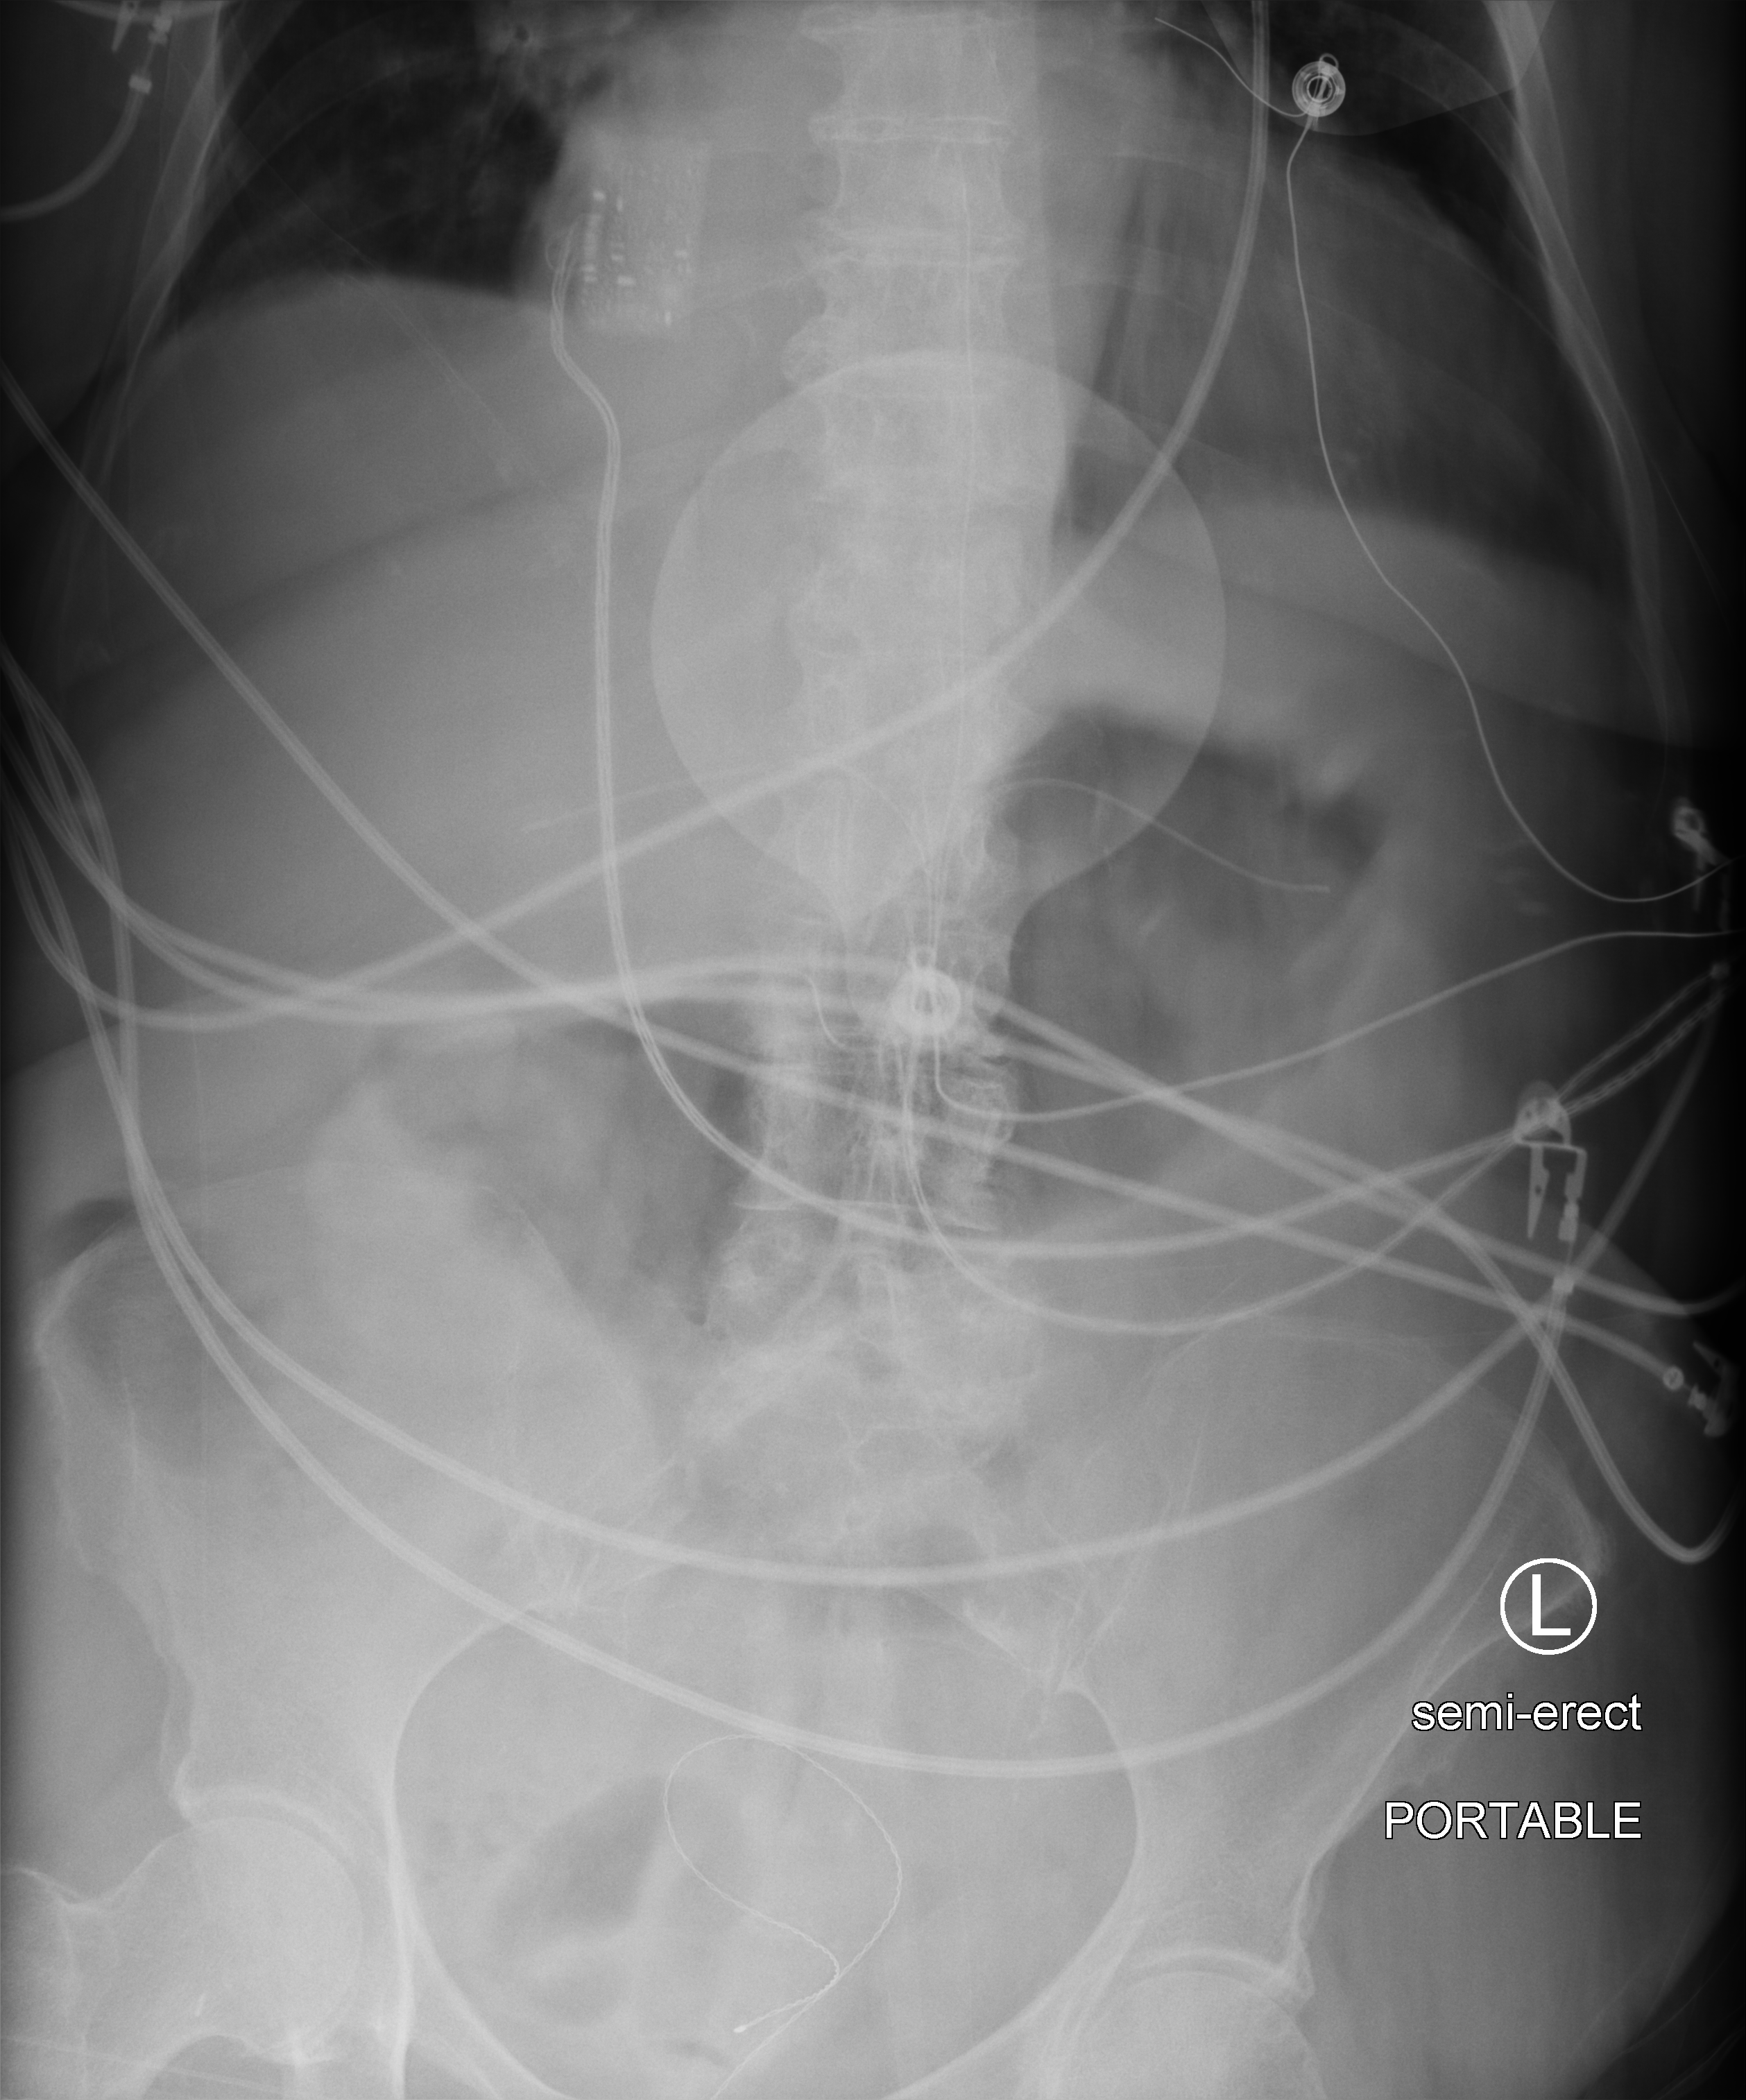
Portable abdomen radiograph. Patient hospitalised with COVID-19; female, aged 75–90 years.
Hospital-stay facts (about this admission, not read from this image; timing relative to this image not recorded):
- mechanically ventilated during this hospital stay: no
- admitted to intensive care during this hospital stay: yes
- chronic kidney disease (admission record): no